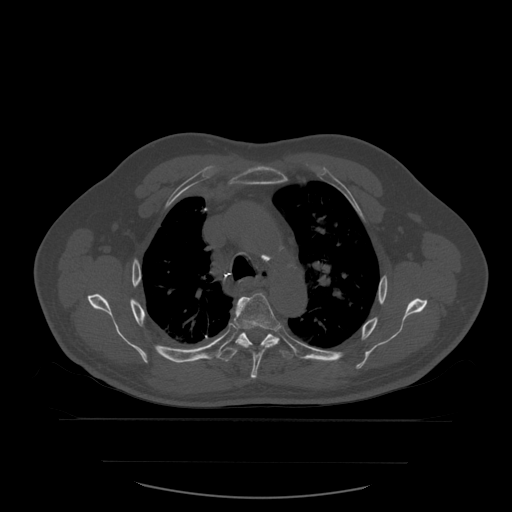
CT including the spine, one axial slice; slice 417 of 590 in the series (ordered by position); bone window (W 1800 / L 400 HU); 1.25 mm slice thickness; 512 × 512 image matrix, field of view 479 × 479 mm. Patient age 71 years. From the clinical record (not read from this slice): primary cancer: lung.
Structures marked on this image (semi-automatically segmented with operator editing):
- T5 vertebra: bounding box (x1, y1, x2, y2) in pixels: (234, 293, 280, 379)
- T6 vertebra: (220, 328, 294, 362)